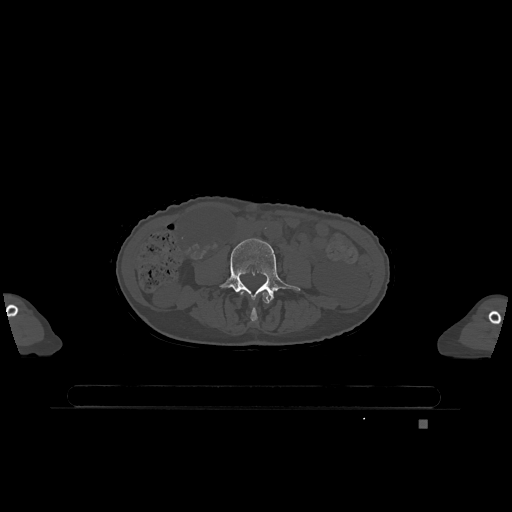
CT including the spine, one axial slice; slice 306 of 1317 in the series (ordered by position); bone window (W 1800 / L 400 HU); 0.5 mm slice thickness; 512 × 512 image matrix, field of view 500 × 500 mm. Patient: female, 74 years. Case-level facts recorded for this patient, not image findings: primary cancer: lung; vertebrae with lytic lesions (as recorded): T1, T4, T5, T6, L4, L5.
Outlined on this slice (semi-automatic segmentation, software-assisted and operator-edited):
- L3 vertebra: bounding box [x1, y1, x2, y2] px = [240, 290, 271, 322]
- L4 vertebra: [219, 238, 300, 300]